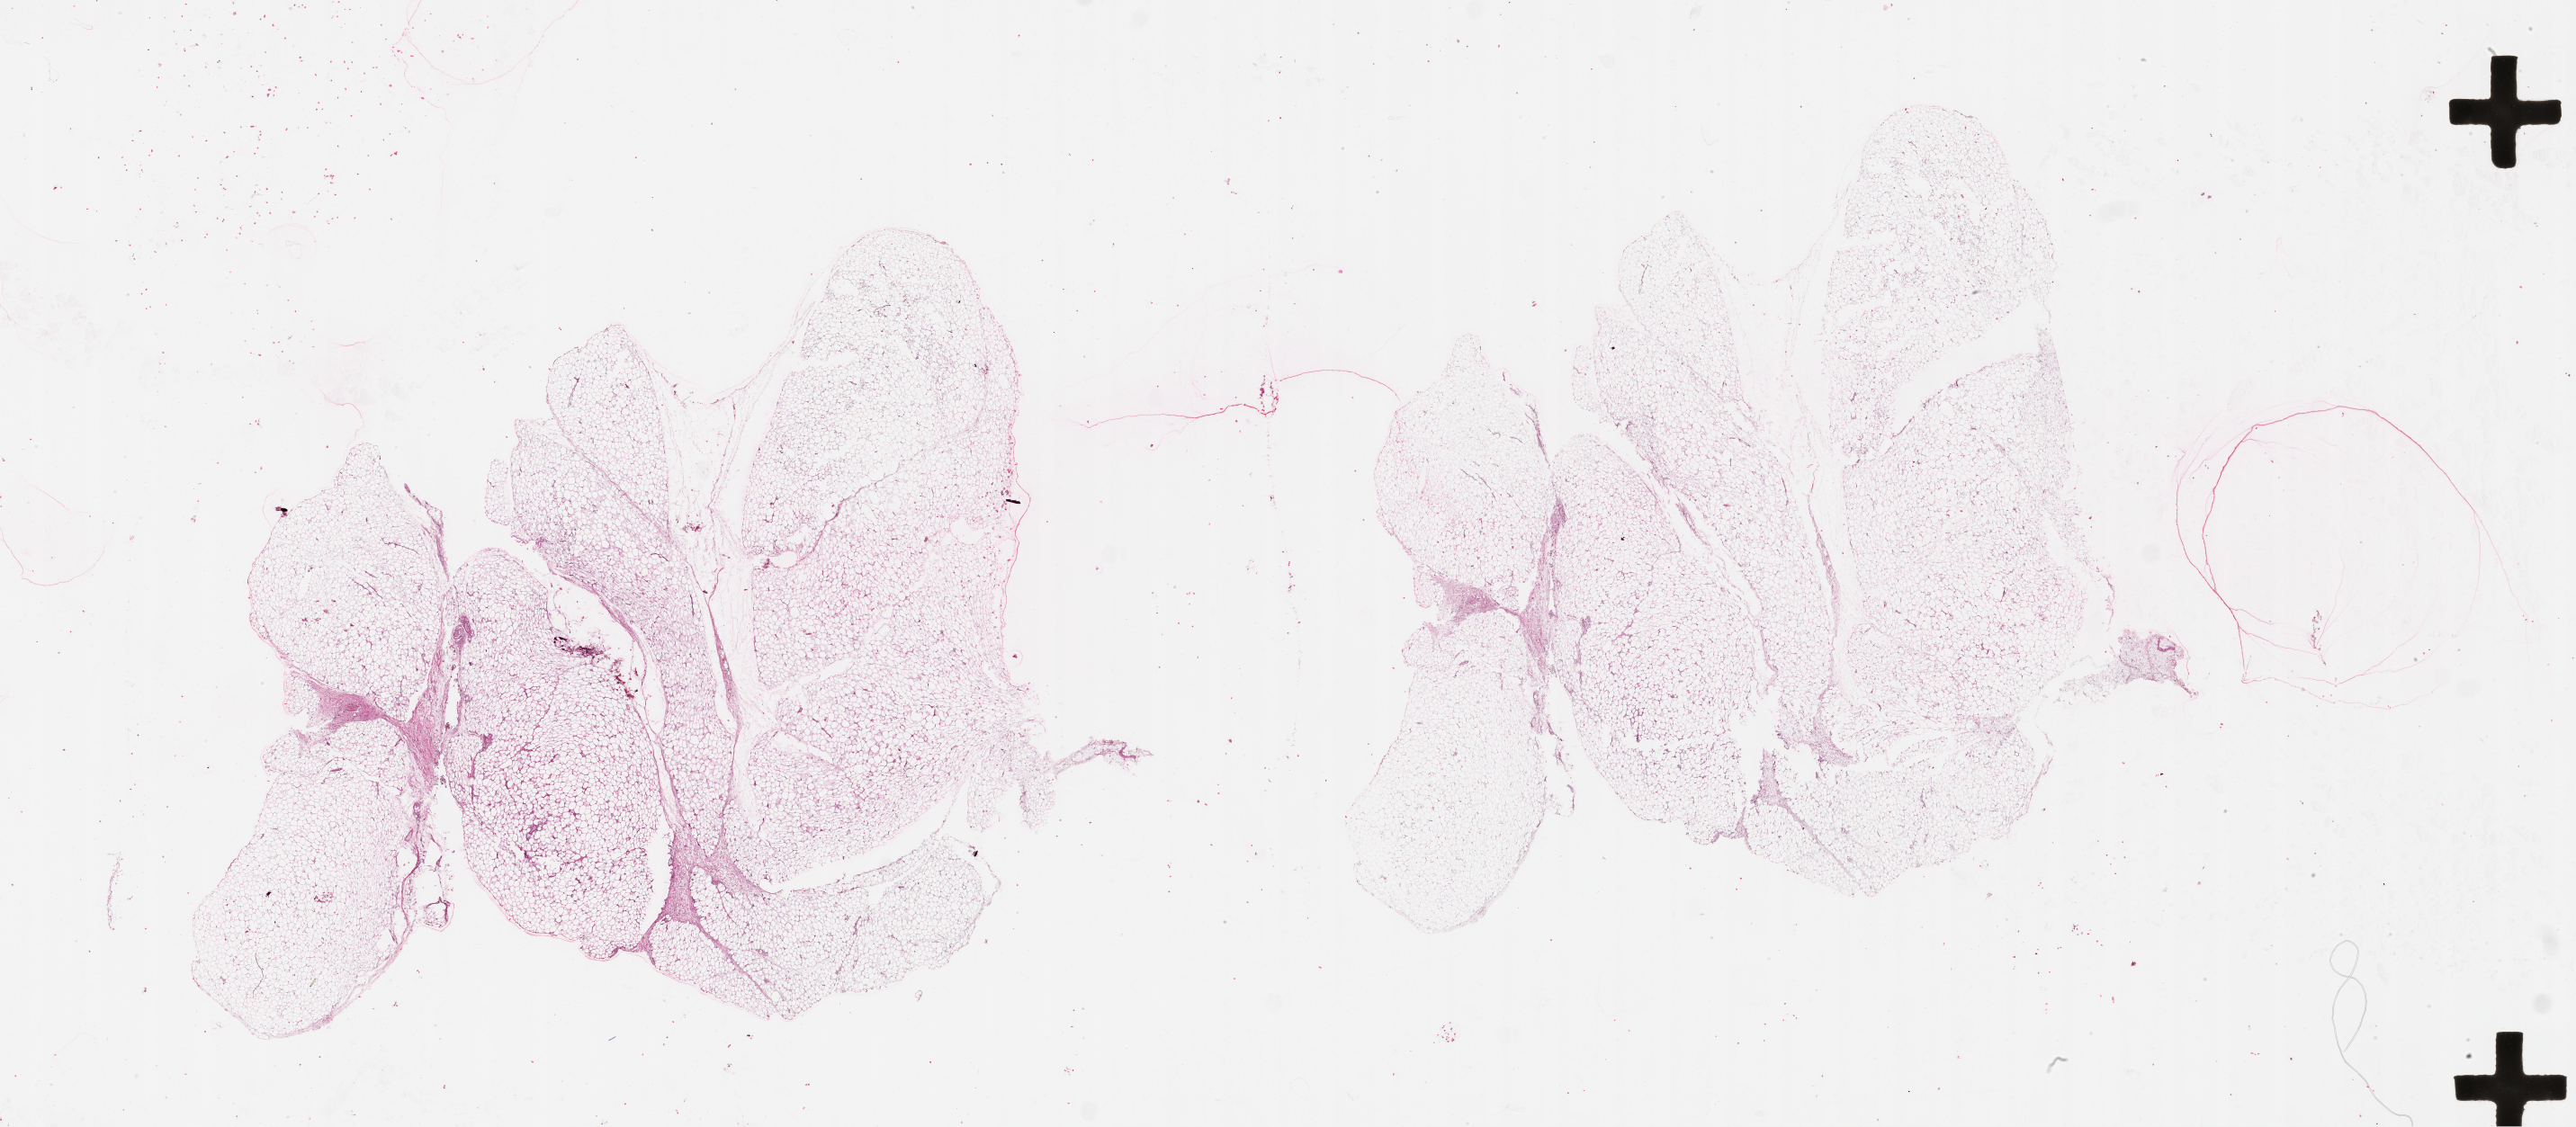
Whole-slide histology image, H&E-stained — whole scanned area (about 46.1 x 20.2 mm) shown as a low-resolution overview. 76-year-old female patient.
- patient diagnosis: Malignant melanoma, NOS